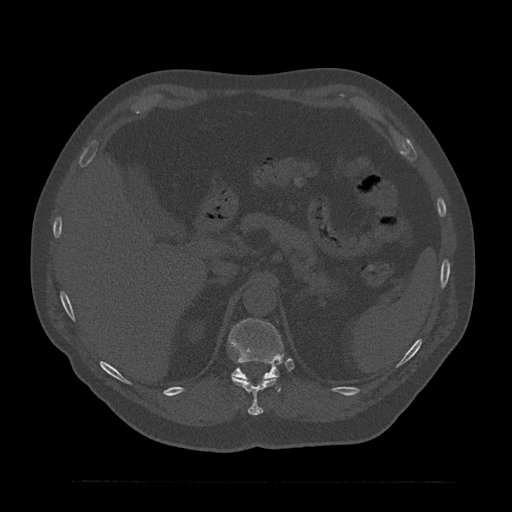
CT including the spine, one axial slice; slice 261 of 797 in the series (ordered by position); bone window (W 1800 / L 400 HU); 0.5 mm slice thickness; 512 × 512 image matrix. Male patient, age 61 years. Case-level facts recorded for this patient, not image findings: primary cancer: prostate.
Outlined on this slice (semi-automatic segmentation, software-assisted and operator-edited):
- T11 vertebra: bounding box (x1, y1, x2, y2) in pixels: (231, 375, 278, 416)
- T12 vertebra: (229, 319, 284, 392)